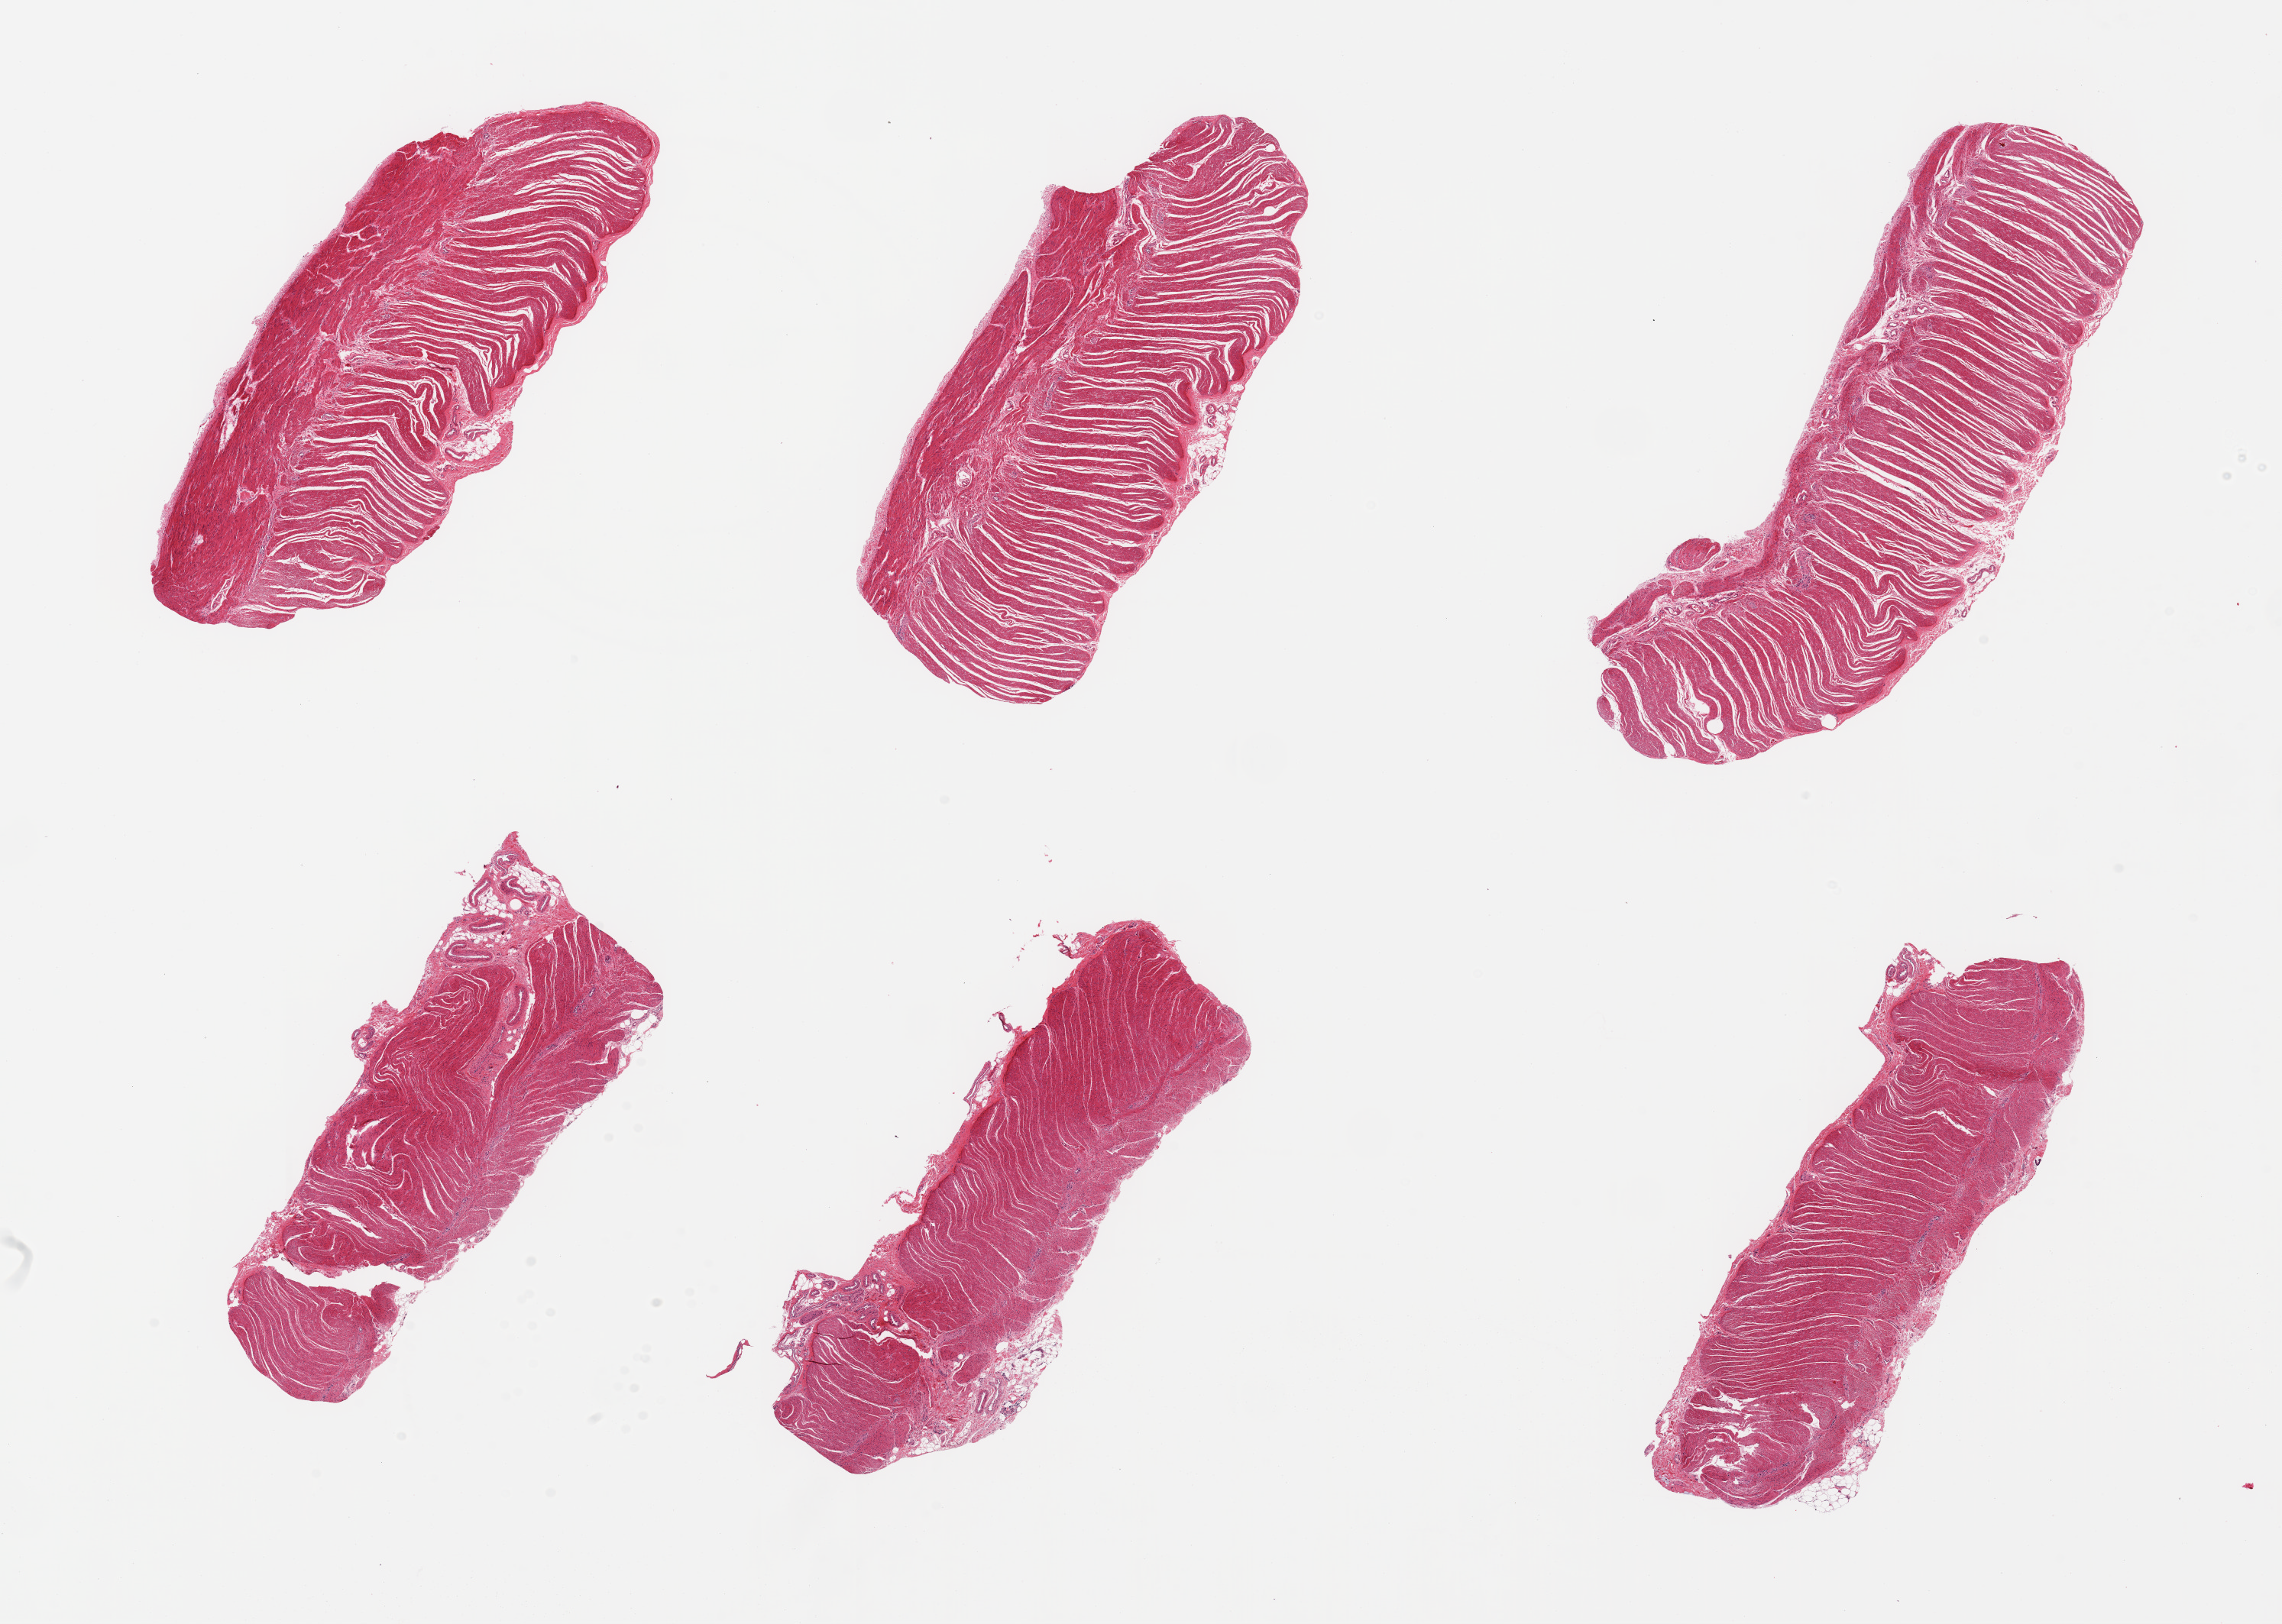
Hematoxylin and eosin (H&E) whole-slide image — whole scanned area (about 23.6 x 16.8 mm) shown as a low-resolution overview; PAXgene-fixed, paraffin-embedded tissue; target tissue: sigmoid colon; donor tissue sample. Male donor.
Review note (as recorded): 6 pieces; well trimmed target muscularis.